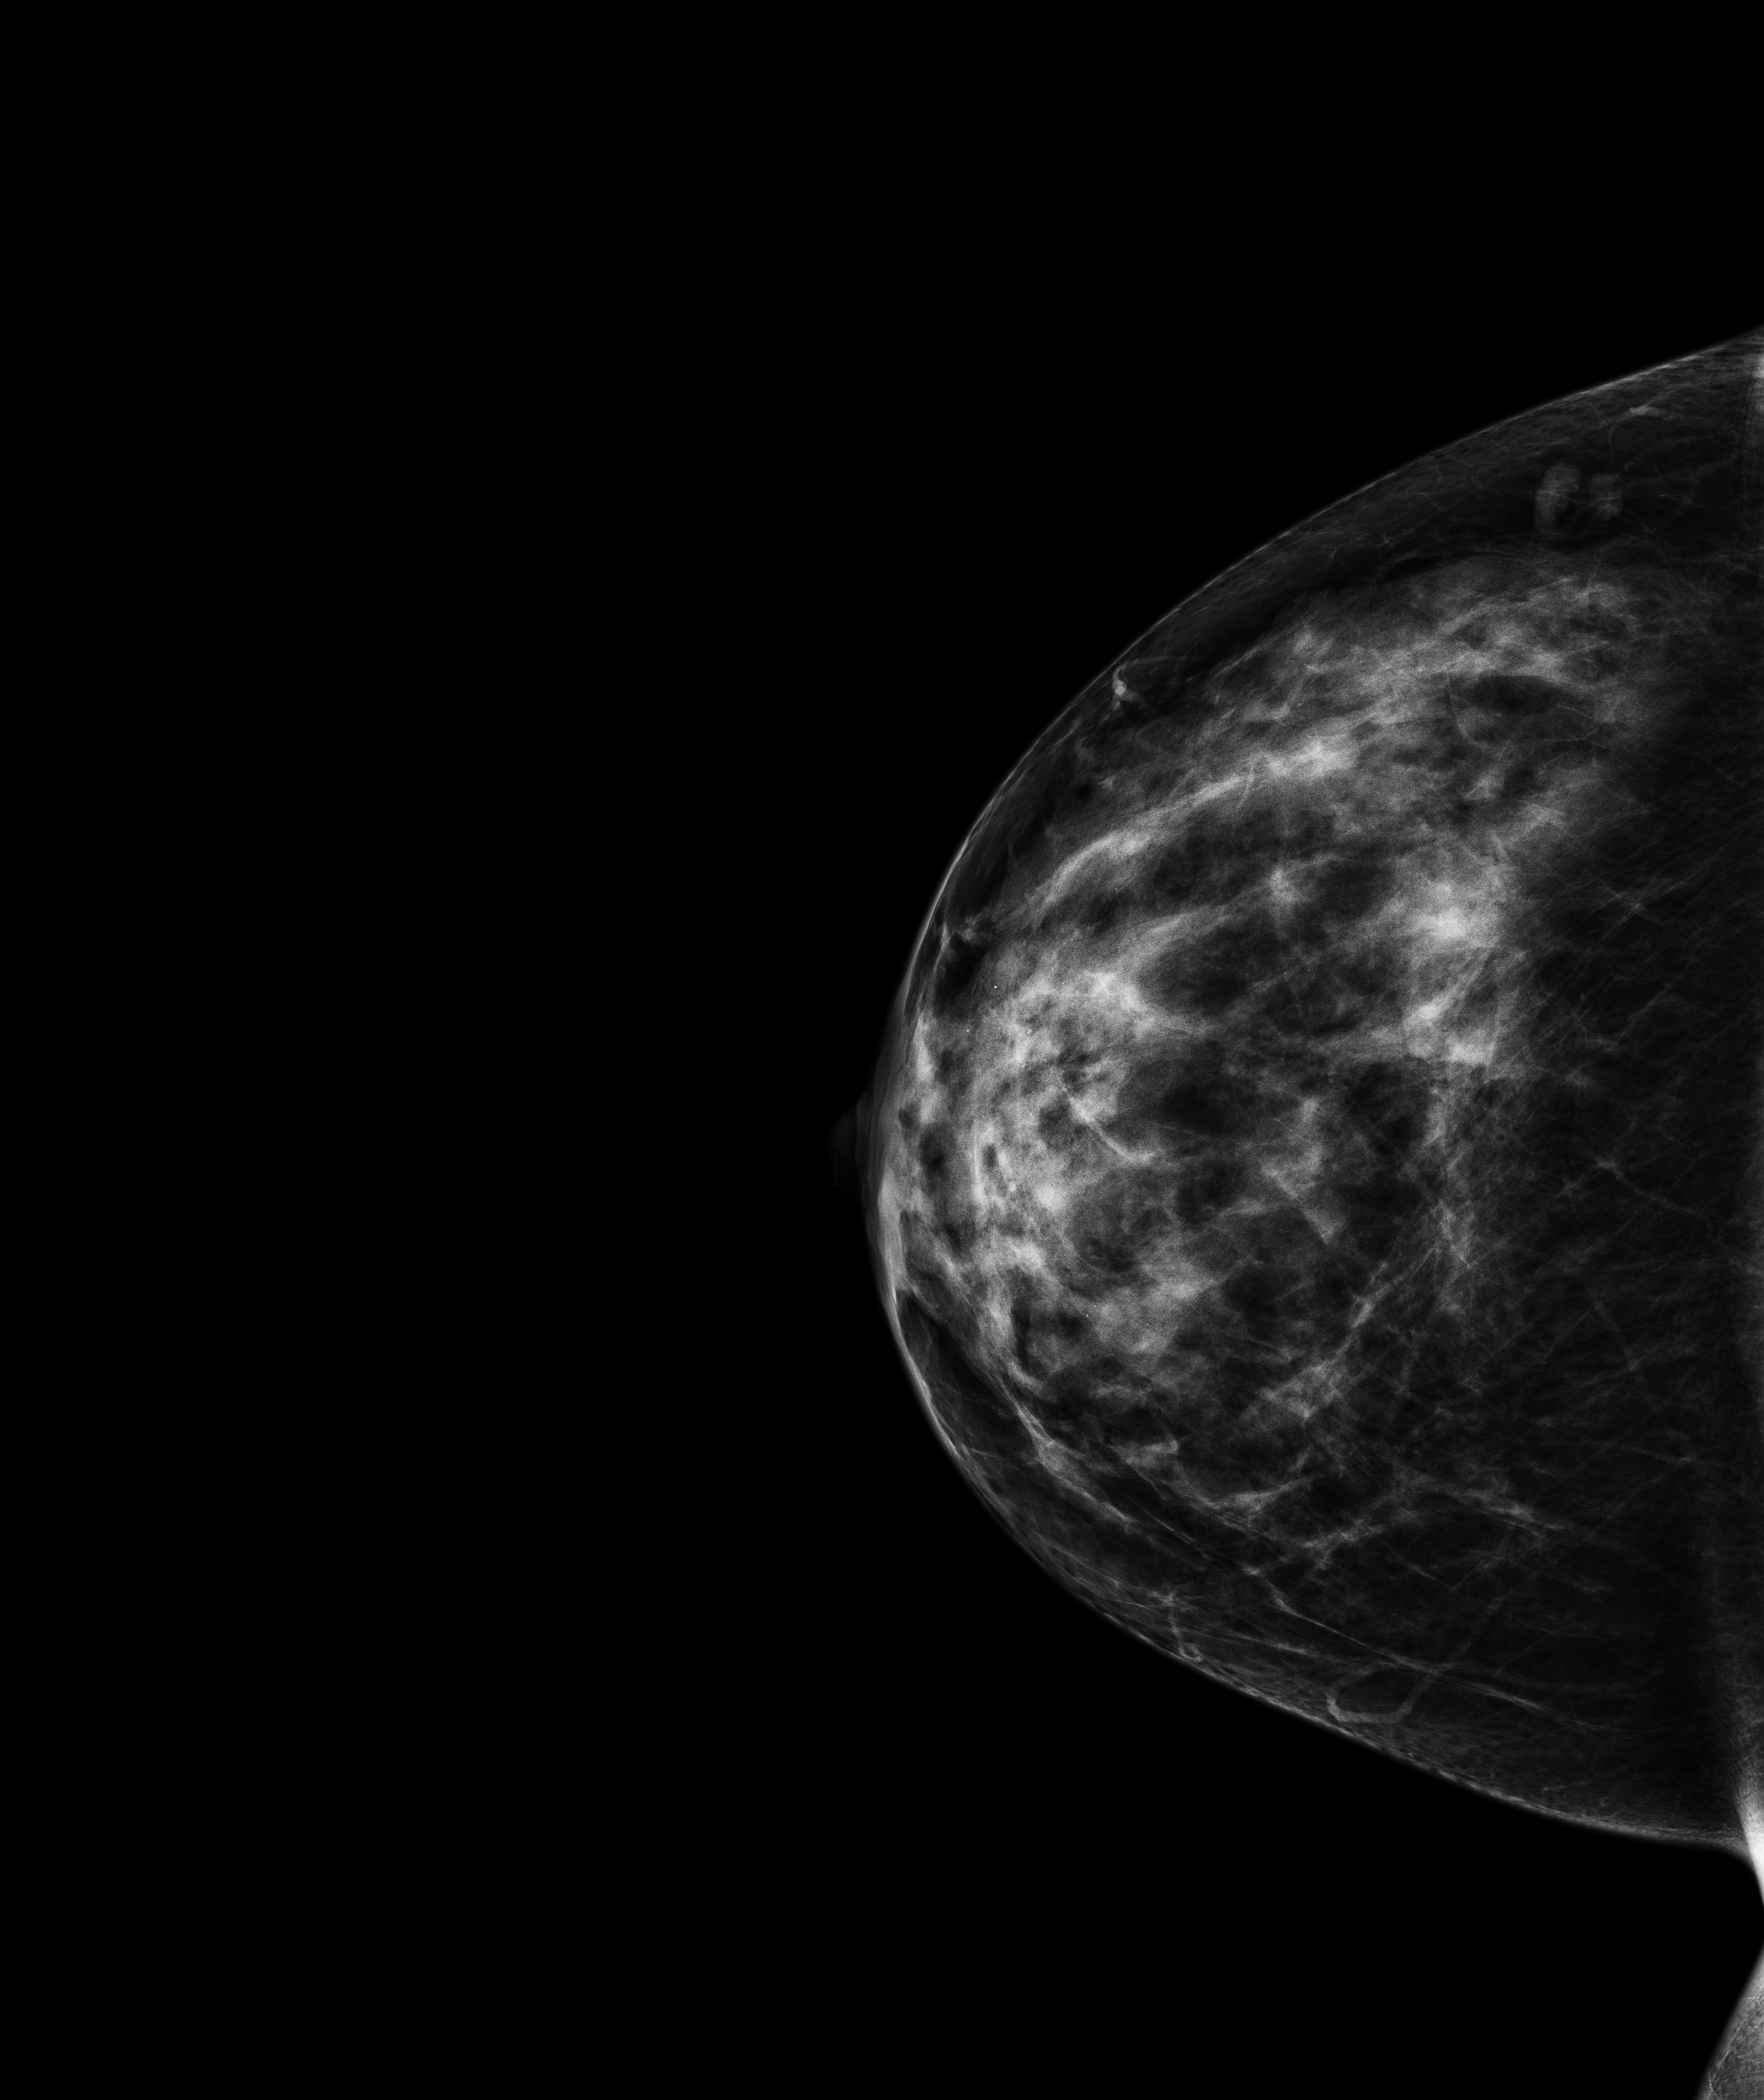
Screening examination, compressed breast thickness 54.7 mm. Patient aged 47 years (female).
Image type: full-field digital mammogram. Breast: right. Projection: cranio-caudal projection.